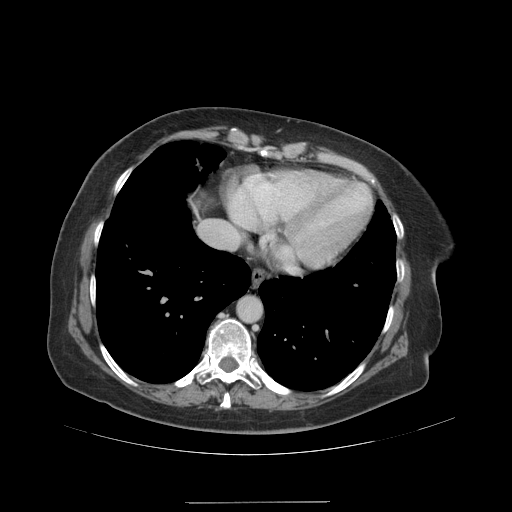
Contrast-enhanced abdominal CT (liver protocol), one axial slice. Slice 90 of 99 in the series (ordered by position). Soft-tissue window (W 400 / L 40 HU). 512 × 512 image matrix, field of view 440 × 440 mm. Case-level facts recorded for this patient, not image findings: diagnosis: hepatocellular carcinoma (patient treated with transarterial chemoembolisation; whether this scan precedes or follows treatment is not stated here); TNM stage (as recorded): Stage-IVA; Child-Pugh class: A; tumour nodularity: multinodular.
Structures marked on this image (semi-automatically segmented with operator editing):
- liver parenchyma outside the tumour (the mass and vessels are separate outlines, so this box may not span the whole liver): bounding box <192,205,198,215> (left, top, right, bottom; pixels)